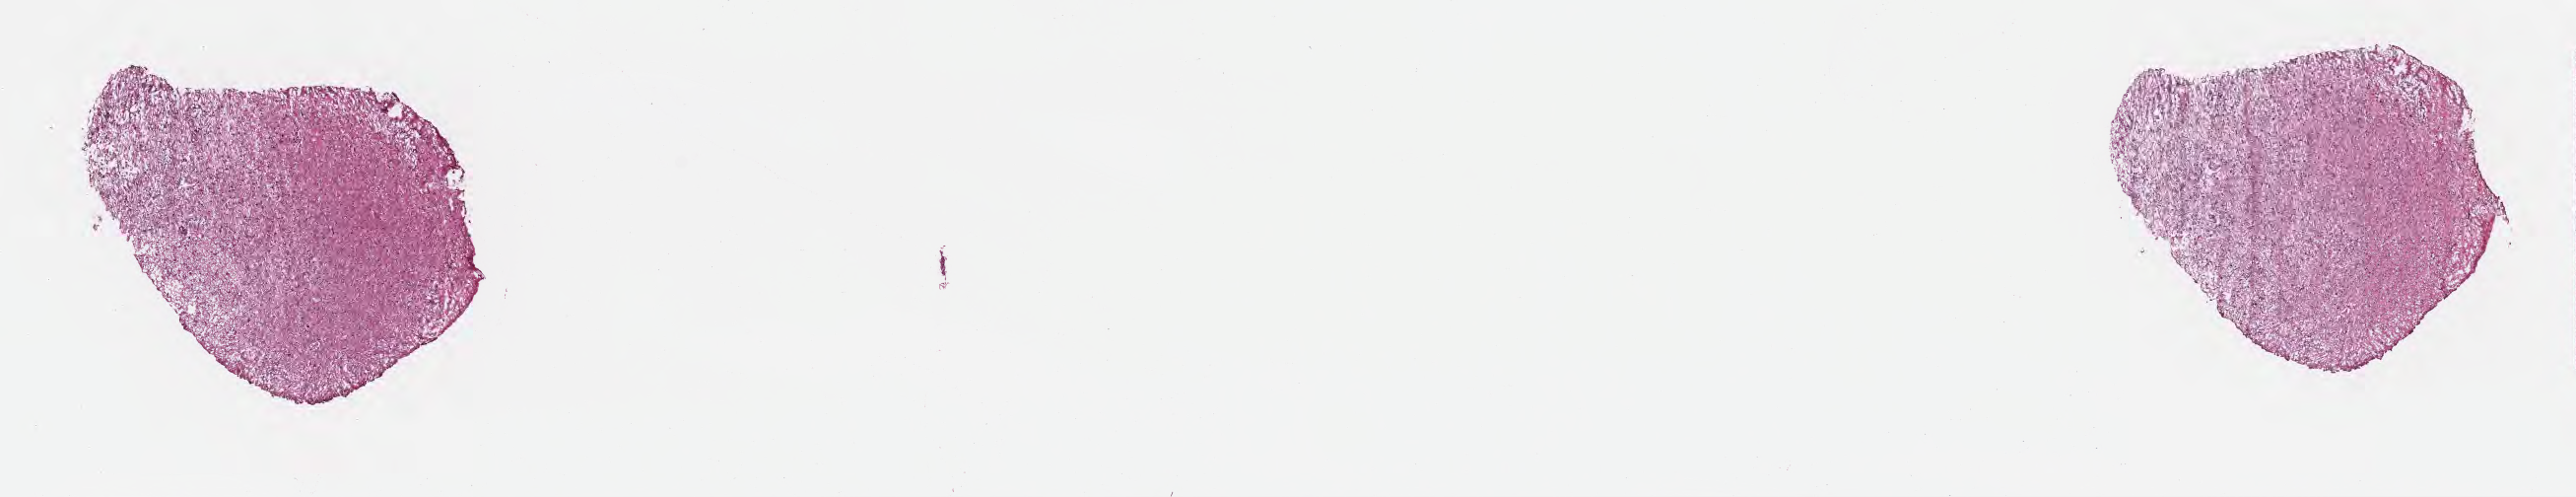
Haematoxylin and eosin whole-slide image, a low-resolution overview of the entire scanned area, about 21.1 x 4.1 mm. Frozen section (tissue freezing medium). Primary tumor. Anatomic site: brain. Male, age 69 years at initial diagnosis. Composition of this section per pathologist review: tumor cells 28%, tumor nuclei 64%, stromal cells 56%, necrosis 0%, normal cells 16%. Inflammatory infiltration, as recorded: lymphocyte infiltration 0%, monocyte infiltration 0%, neutrophil infiltration 0%.
* histologic diagnosis: Glioblastoma, NOS